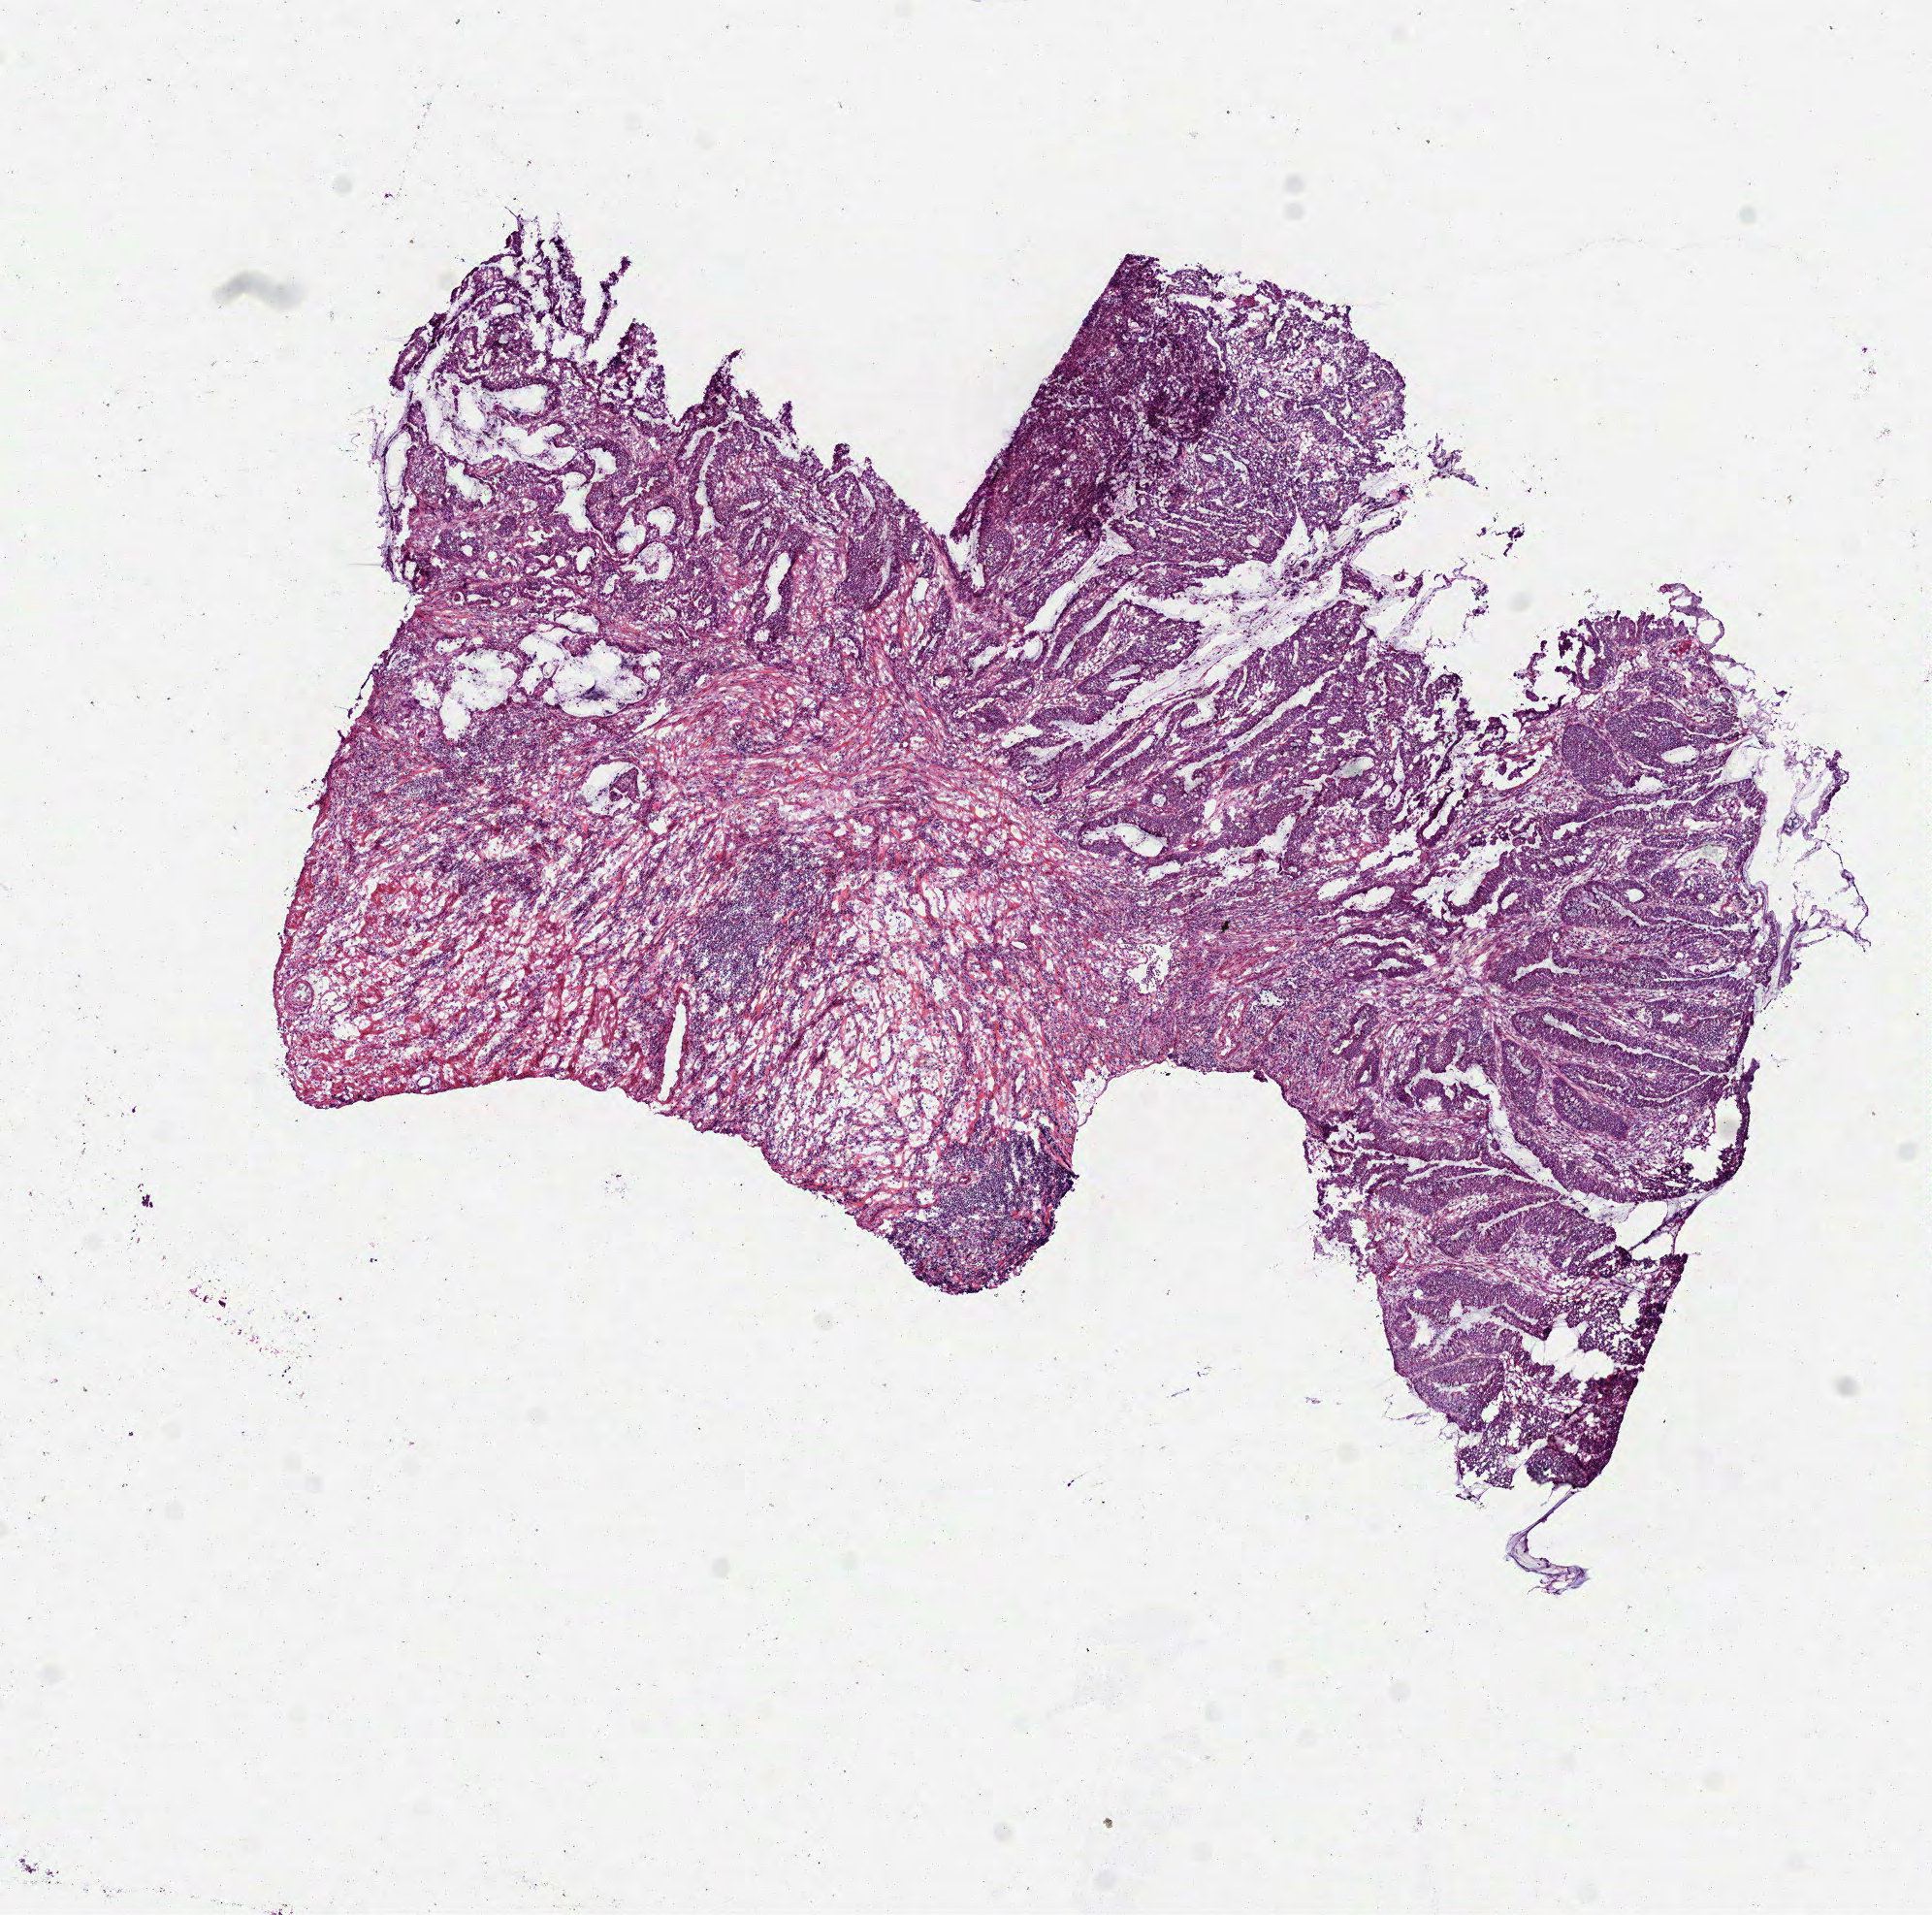
Digitized H&E tissue section (whole slide) — a low-resolution overview of the entire scanned area, about 8.0 x 8.0 mm (slide scanned at 40x). Frozen section. Sample: primary tumour, colon. Patient sex: female. Slide review estimates, as recorded: tumour cells 70%, tumour nuclei 70%, normal cells 0%, stromal cells 30%, necrosis 0%.
• diagnosis: Mucinous adenocarcinoma (ascending colon)
• AJCC pathologic stage: I (5th edition)